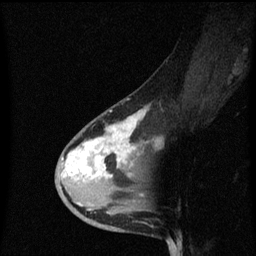
Breast MRI (dynamic contrast-enhanced), one sagittal slice; position 33 of 60 along the scan axis; dynamic contrast-enhanced series, image 2 of 3 at this slice position (ordered by acquisition); 1.5 T; TE 4.2 ms, TR 8.4 ms; 2 mm slice thickness; 256 × 256 image matrix, field of view 200 × 200 mm. Female patient, age 38 years. From the clinical record (not read from this slice): setting: breast cancer imaged before/during neoadjuvant chemotherapy; receptor status: HR-positive, HER2-negative.
Structures marked on this image (semi-automatically segmented with operator editing):
- analysis volume of interest (the breast-tissue region the enhancement analysis was run in; not a lesion): bounding box (x1, y1, x2, y2) in pixels: (56, 100, 149, 205)
- tumour enhancement mask (voxels above the 70 % enhancement threshold inside the analysis volume of interest): (62, 110, 145, 177)